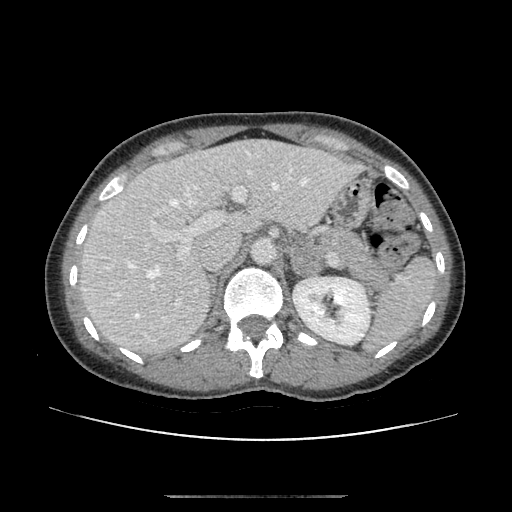
Contrast-enhanced abdominal CT, one axial slice; position 70 of 179 along the scan axis; 120 kVp; soft-tissue window (W 400 / L 40 HU); 2.5 mm slice thickness; 512 × 512 image matrix, field of view 360 × 360 mm. Female patient, age 51 years. Case-level facts recorded for this patient, not image findings: diagnosis: adrenocortical carcinoma; tumour side: left adrenal; tumour size at pathology: 3.5 cm; Ki-67 index: 45 %; stage (as recorded): 1.
Structures marked on this image (semi-automatically segmented with operator editing):
- mass: bounding box (x1, y1, x2, y2) in pixels: (297, 245, 323, 277)